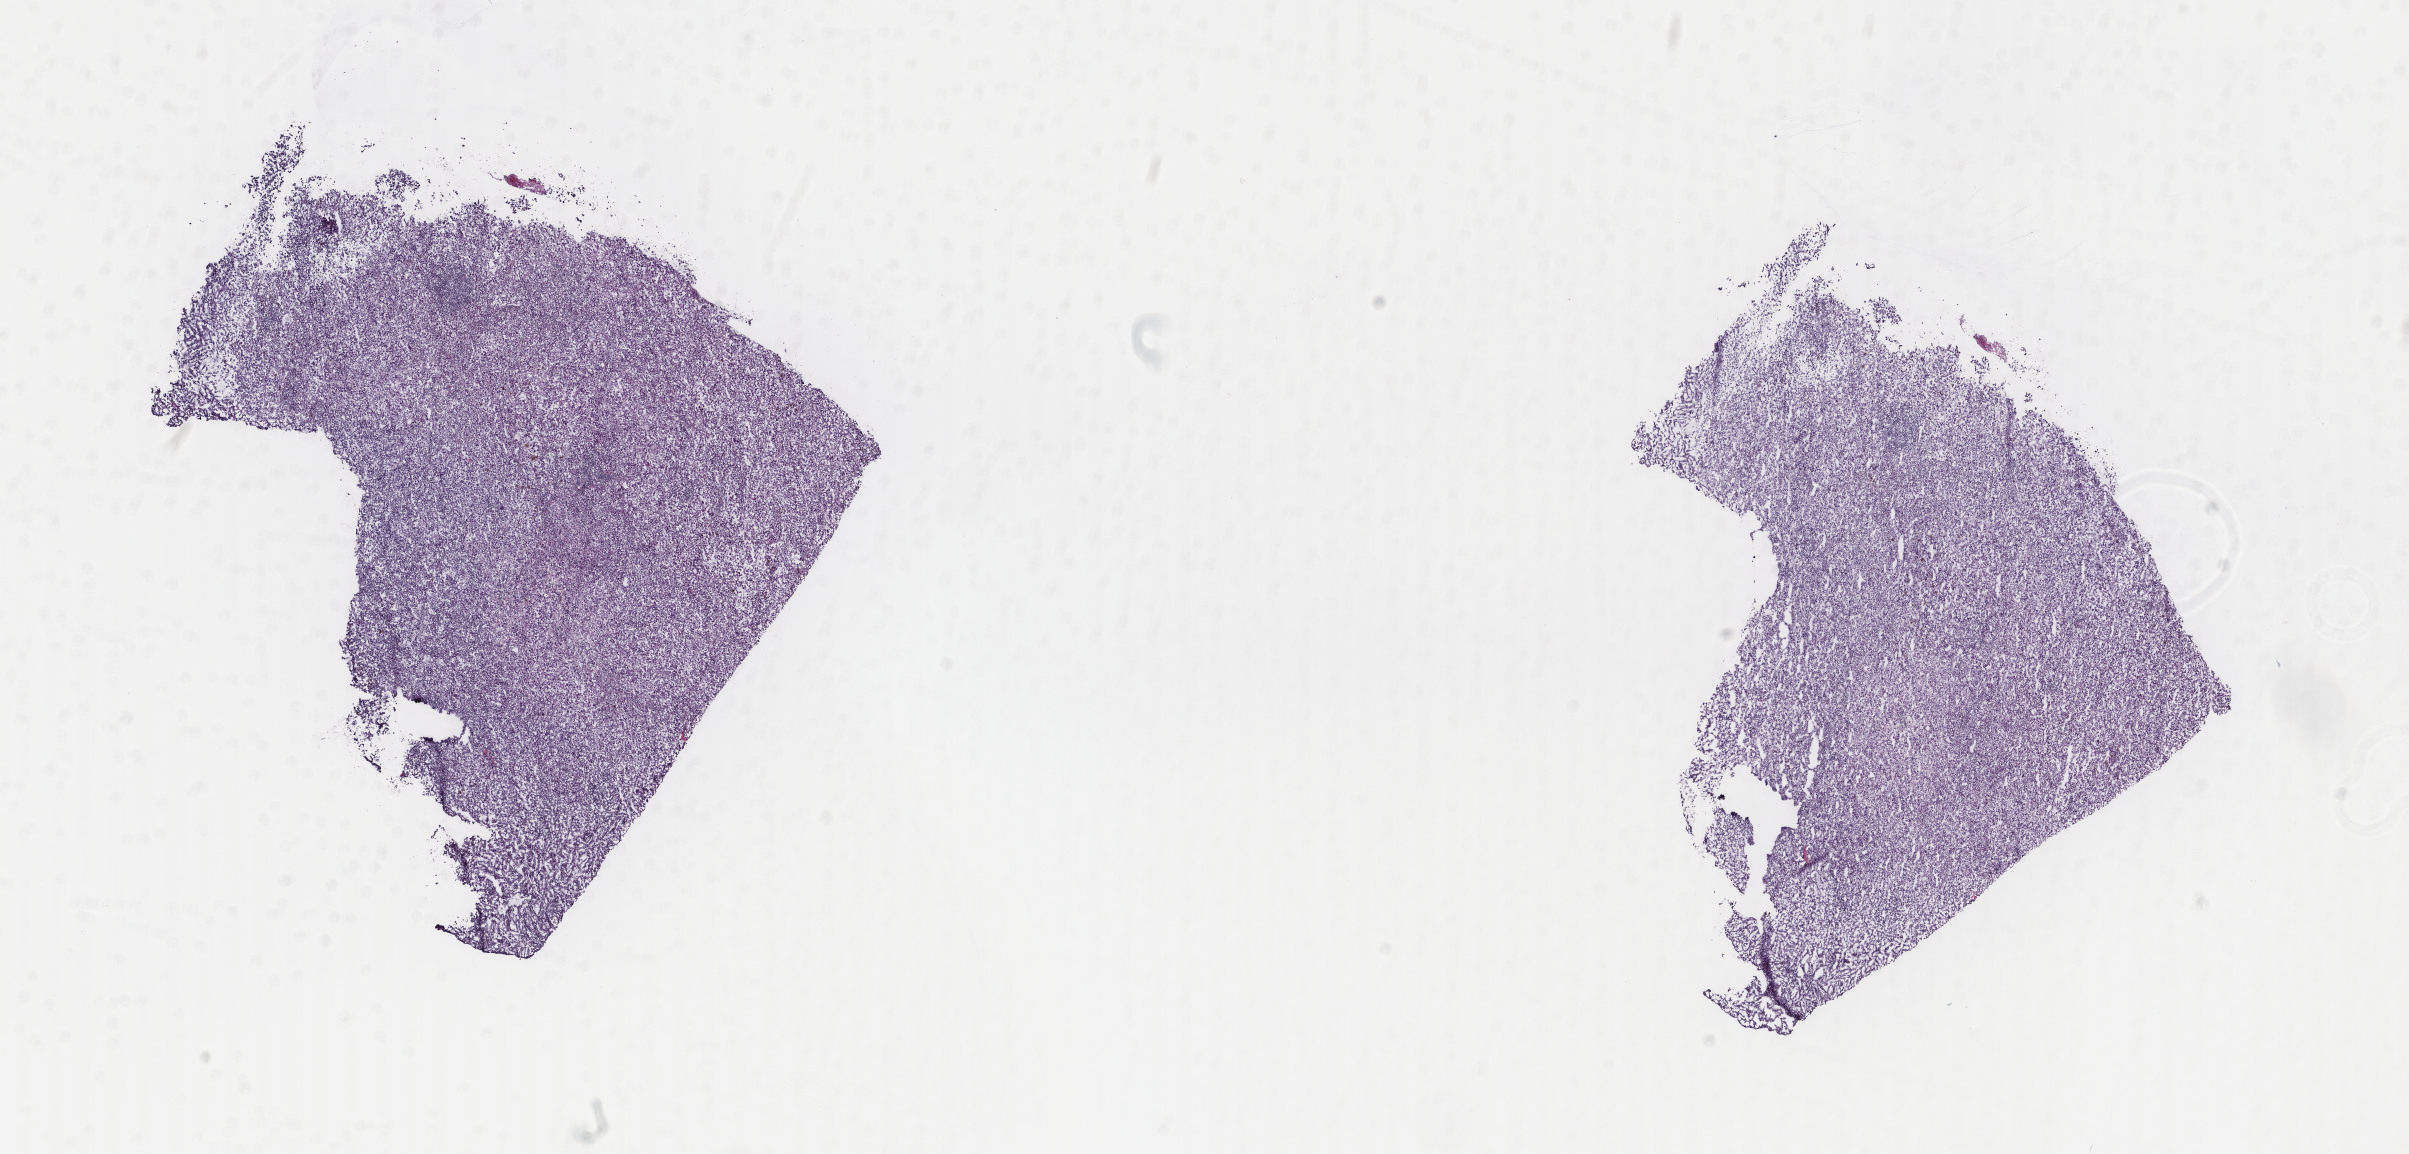
Hematoxylin and eosin (H&E) stained whole-slide image, whole scanned area (about 19.1 x 9.2 mm) shown as a low-resolution overview. Frozen section from the top of the tissue portion. Metastatic tumour sample, sampled site: lymph nodes of inguinal region or leg. Female, age 86 years at initial diagnosis. Slide review estimates, as recorded: tumour cells 100%, tumour nuclei 85%, normal cells 0%, stromal cells 0%, necrosis 0%. Infiltration values recorded for this section: lymphocyte infiltration 0%, monocyte infiltration 0%, neutrophil infiltration 0%.
This section: metastatic tumour tissue. Patient diagnosis: Malignant melanoma, NOS.